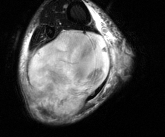
MRI of an extremity soft-tissue mass, one axial slice. Position 39 of 81 along the scan axis. T2-weighted fat-saturated. MR volume resampled by the dataset authors to the PET/CT grid (not the native acquisition matrix). 165 × 137 image matrix, field of view 161 × 134 mm. Male patient. From the clinical record (not read from this slice): histological type: liposarcoma - round cell; grade: high; site of the primary tumour: right calf.
Structures marked on this image (expert contour drawn on MRI and transferred to this co-registered scan by the dataset authors):
- gross tumour volume (mass): bounding box (x1, y1, x2, y2) in pixels: (27, 30, 111, 117)